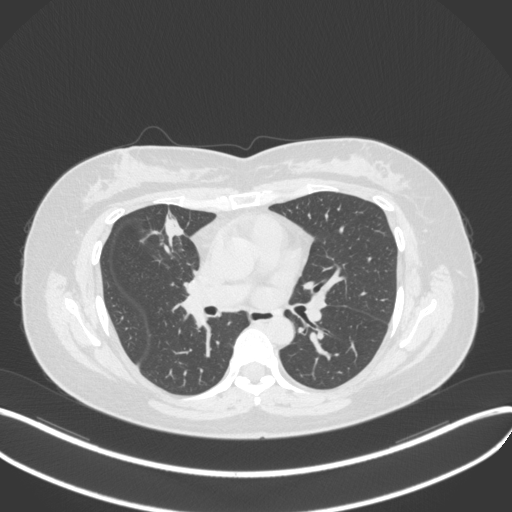
Chest CT, one axial slice; slice 170 of 272 in the series (ordered by position); reconstruction kernel B31f; 120 kVp; lung window (W 1500 / L -600 HU); 512 × 512 image matrix, field of view 400 × 400 mm. Patient: female, 42 years. From the clinical record (not read from this slice): clinical TNM (as recorded): T1b N0 M0.
Structures marked on this image (rectangle marked by the reading radiologist):
- lung tumour (recorded histology: adenocarcinoma): bounding box [x1, y1, x2, y2] px = [158, 212, 187, 250]